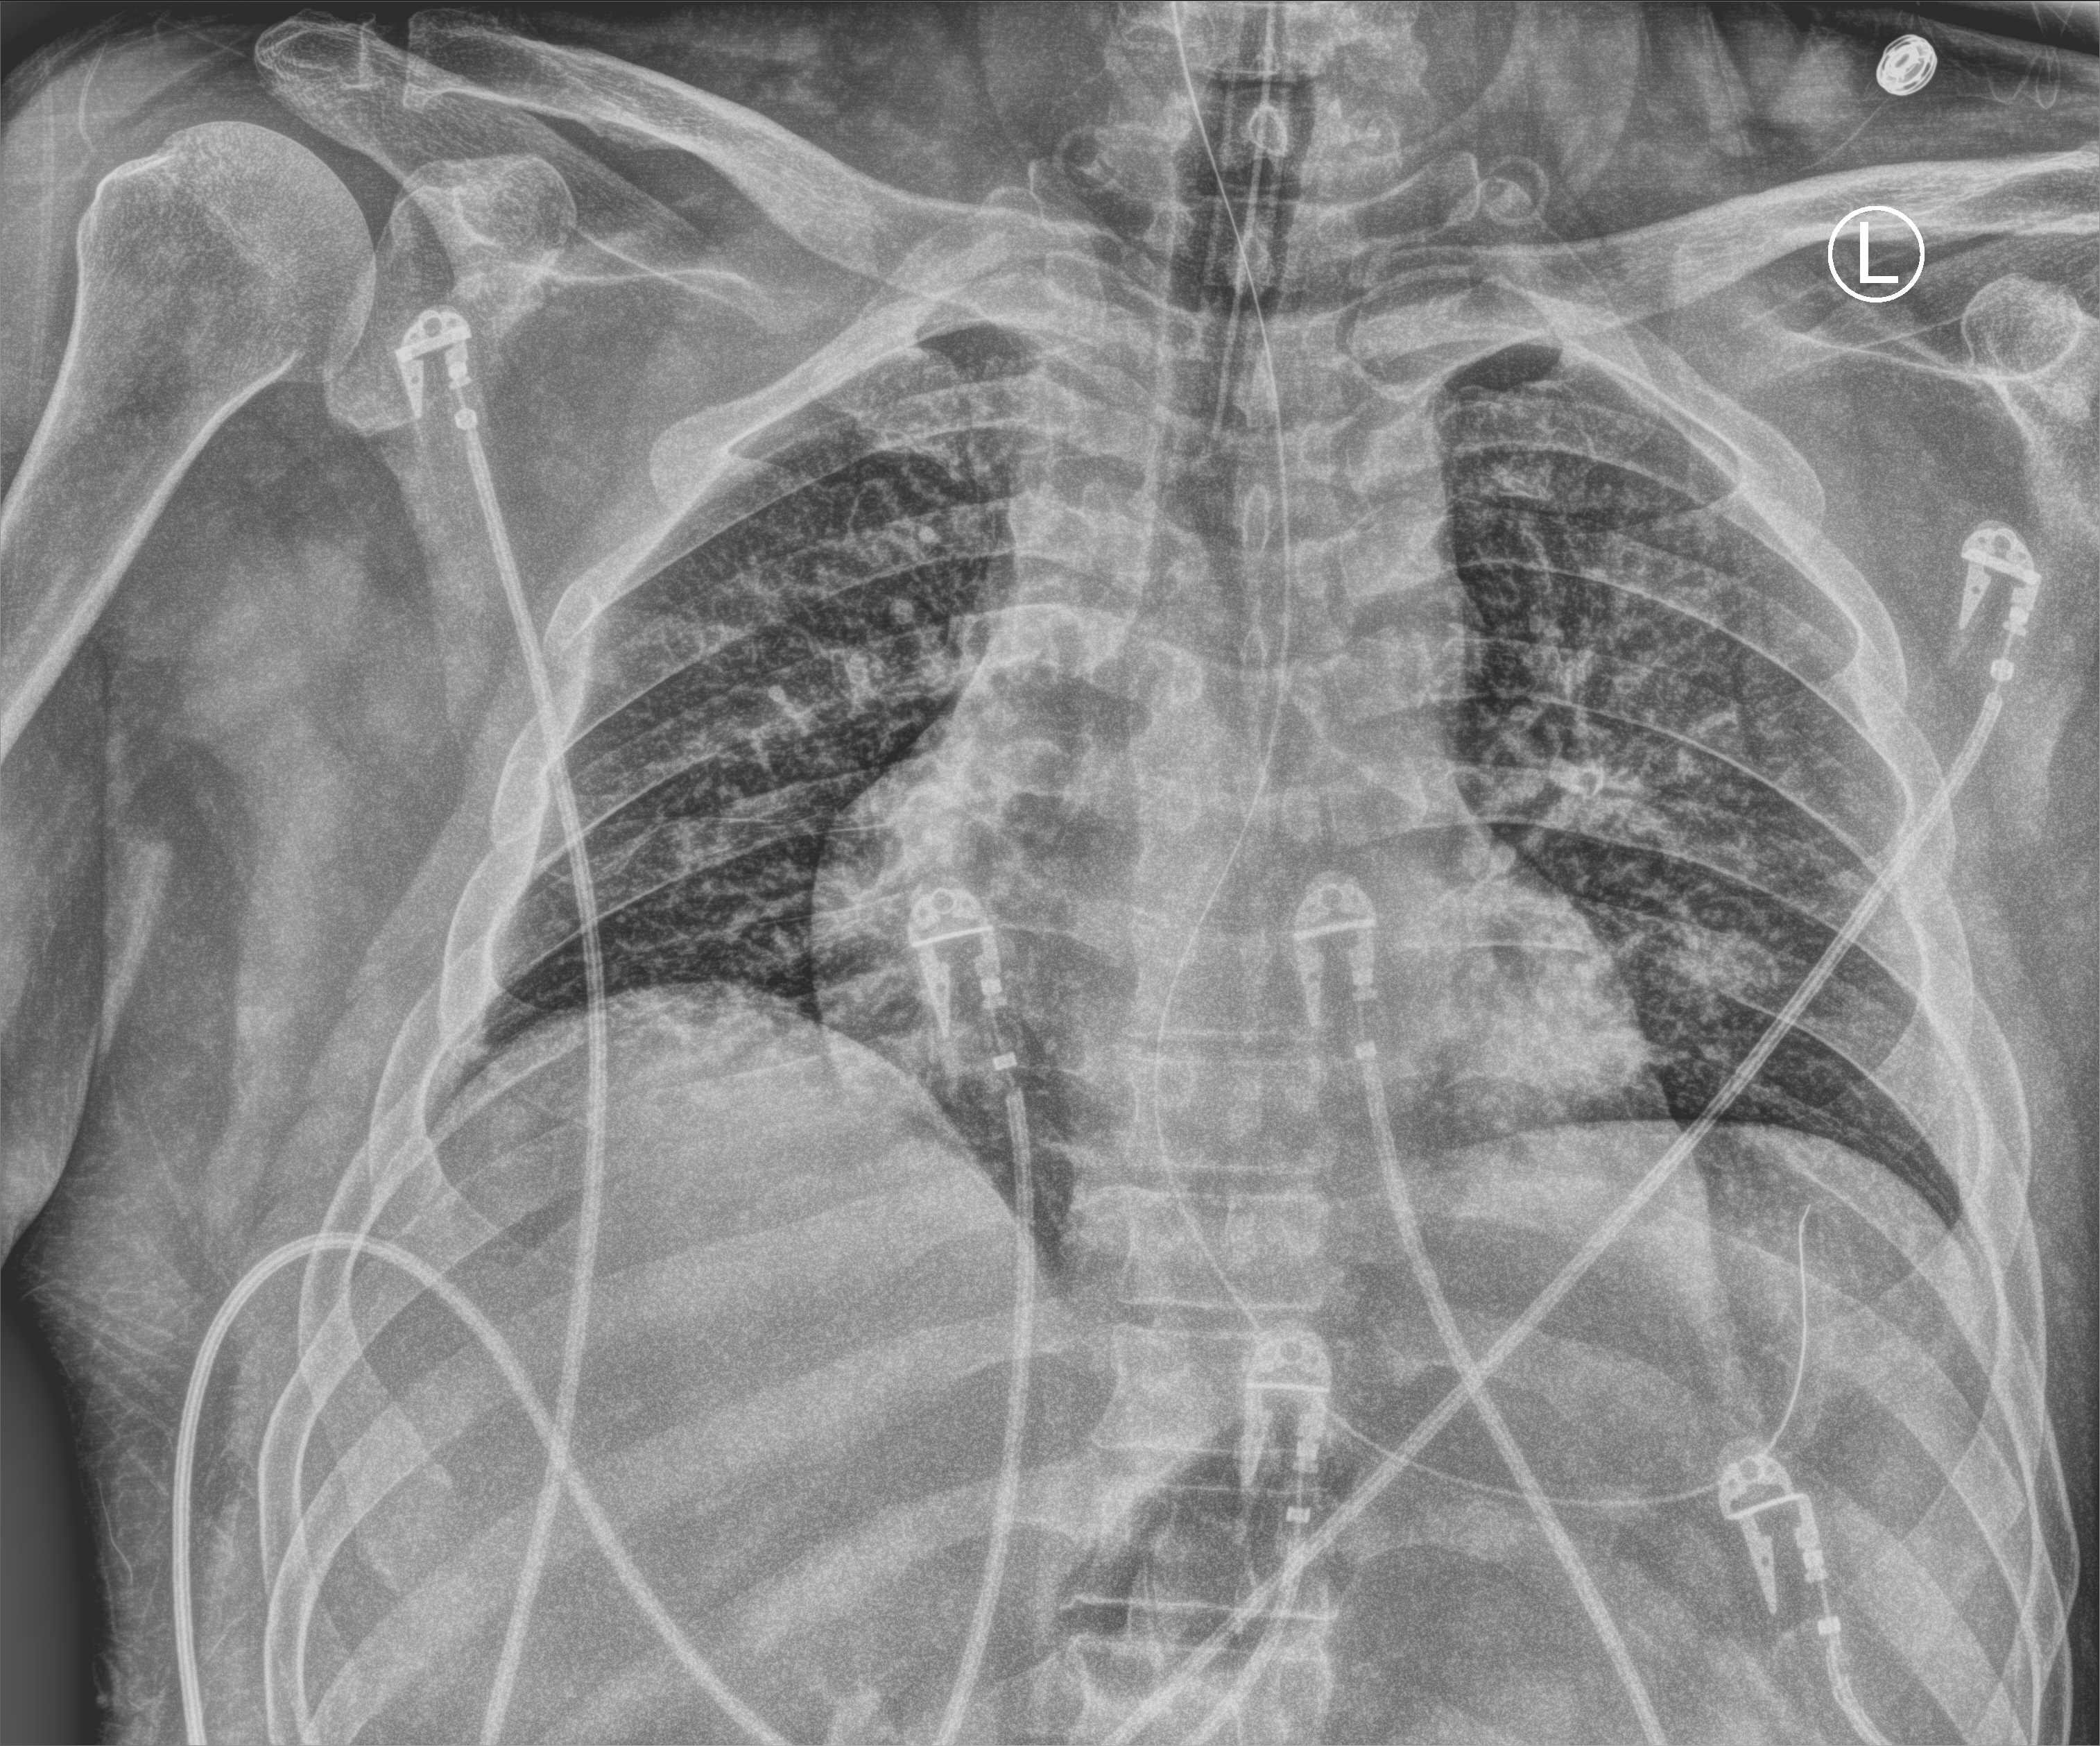
Chest X-ray (portable); anteroposterior (AP) projection. Patient hospitalised with COVID-19; male, aged 18–59 years.
From the hospital-stay record, not from the radiograph (when in the stay this image was taken is not recorded):
- mechanically ventilated during this hospital stay: yes
- admitted to intensive care during this hospital stay: yes